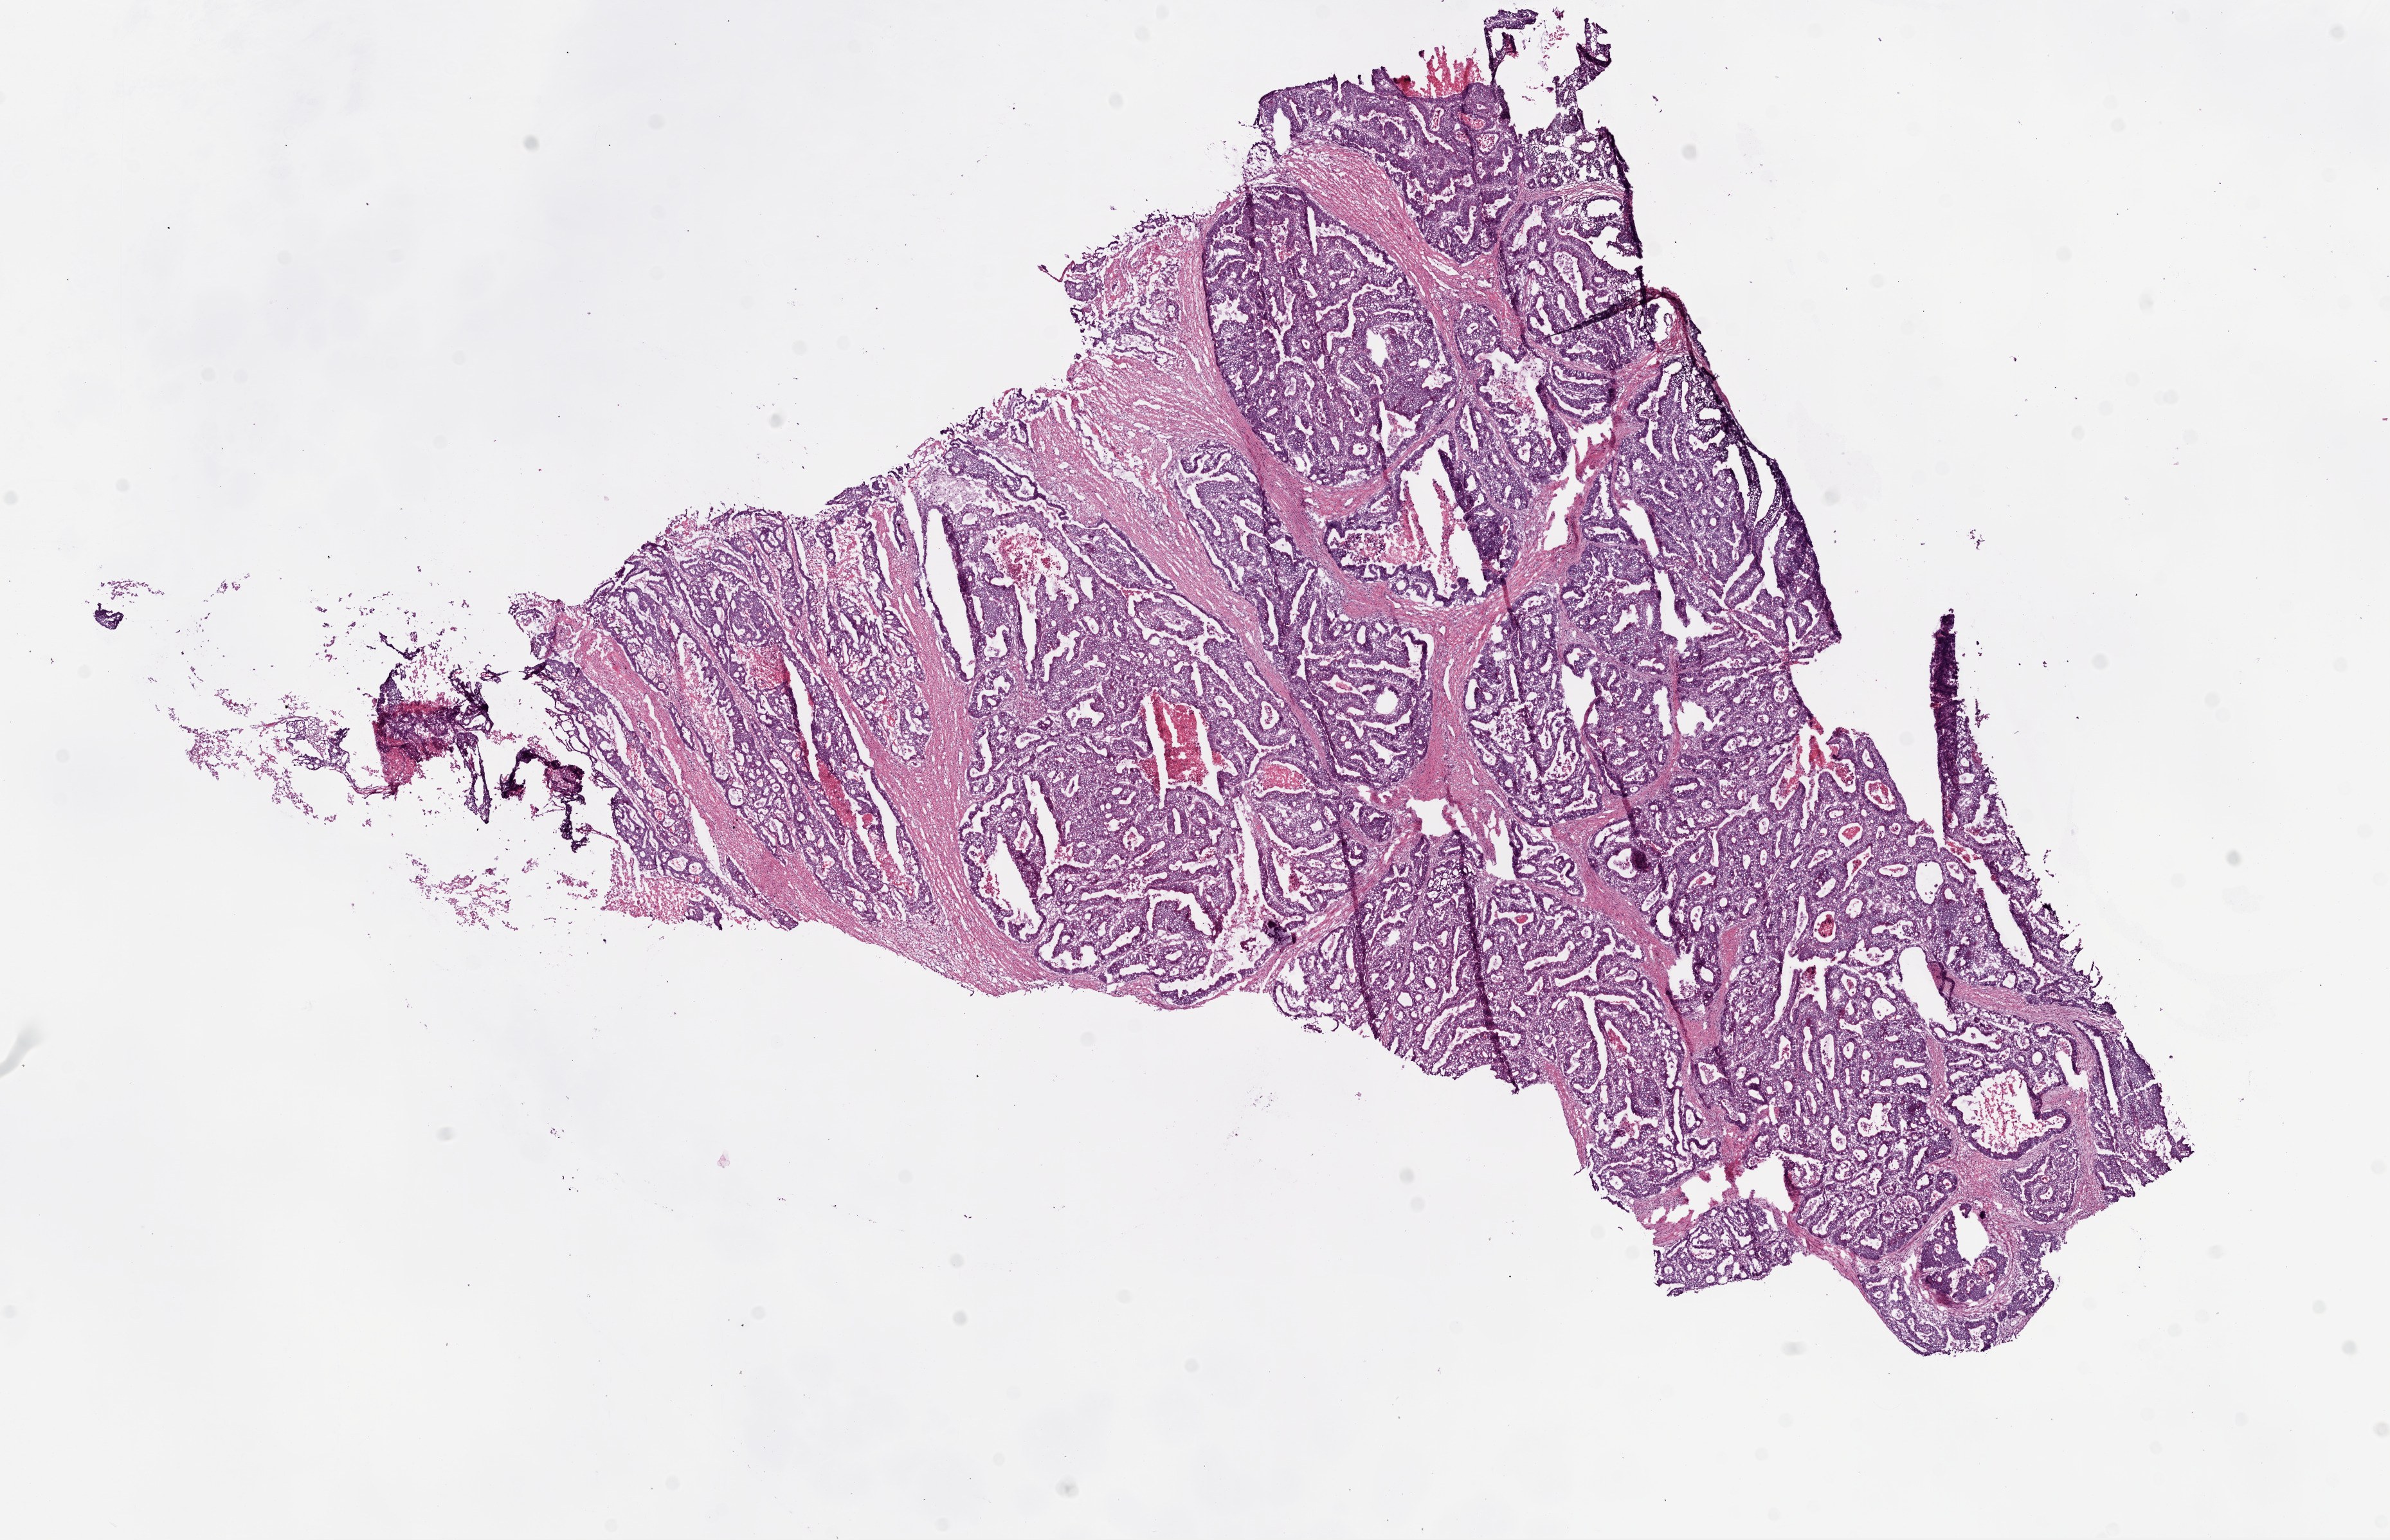
Whole-slide histology image, Hematoxylin and eosin (H&E) stained — whole scanned area (about 15.0 x 9.7 mm, slide scanned at 20x) shown as a low-resolution overview, frozen section, primary tumour sample from the rectum. Male, age 54 years at initial diagnosis. Pathologist review of this section (percent, as recorded): tumour cells 73%, tumour nuclei 80%, normal cells 0%, stromal cells 15%, necrosis 8%.
AJCC pathologic stage: IIB (7th edition). Pathologic diagnosis: Adenocarcinoma, NOS.